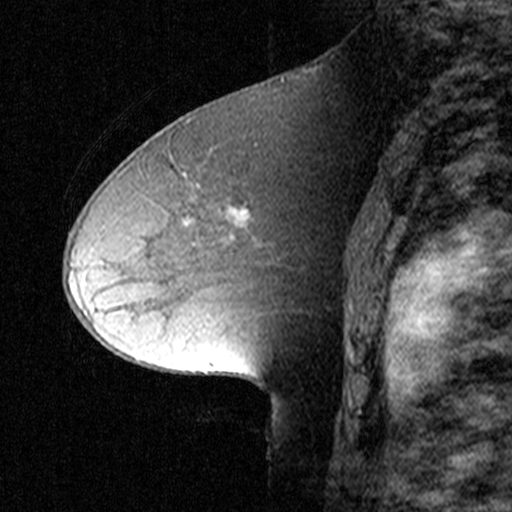
Breast MRI (dynamic contrast-enhanced), one sagittal slice. Position 24 of 44 along the scan axis. Dynamic contrast-enhanced study with each time point stored as its own series, time point 2 of 3 at this slice position (early post-contrast, ordered by acquisition time). 1.5 T. TE 4.5 ms, TR 11 ms. 3 mm slice thickness. 512 × 512 image matrix, field of view 200 × 200 mm. Patient: female, 50 years. Case-level facts recorded for this patient, not image findings: setting: breast cancer imaged before/during neoadjuvant chemotherapy; receptor status: HR-positive, HER2-negative.
Annotated regions visible in this slice (semi-automatically segmented with operator editing):
- analysis volume of interest (the breast-tissue region the enhancement analysis was run in; not a lesion): bounding box (x1, y1, x2, y2) in pixels: (154, 164, 313, 287)
- tumour enhancement mask (voxels above the 90 % enhancement threshold inside the analysis volume of interest): (230, 209, 246, 220)